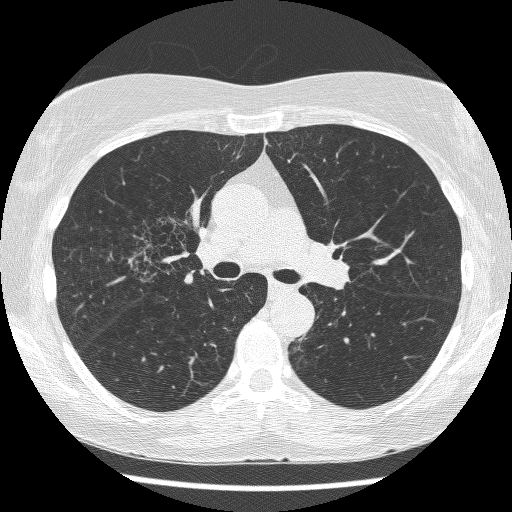
Chest CT (low-dose screening protocol), one axial image, baseline annual screen, lung window (W 1500 / L -600 HU), lung (sharp) reconstruction kernel (BONE), slice 171 of 271 in the series. Female participant, aged 64 years at enrolment. Former smoker at enrolment.
- Expert-annotated lung lesion, box from (x=124, y=219) to (x=202, y=285) px.
- The screening reader recorded 3 non-calcified nodules or masses ≥4 mm on this exam; which of them this box marks is not recorded.
- Lung cancer was diagnosed 735 days after this screen: adenocarcinoma, NOS, right upper lobe, right middle lobe, right hilum, stage IV (AJCC 6th edition), 85 mm at pathology.